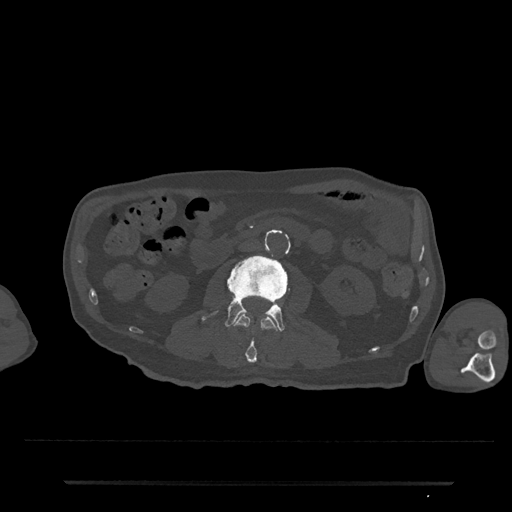
CT including the spine, one axial slice. Position 17 of 797 along the scan axis. Reconstruction kernel Br40s/3. 120 kVp. Bone window (W 1800 / L 400 HU). 512 × 512 image matrix, field of view 427 × 427 mm. Patient: male, 74 years. From the clinical record (not read from this slice): primary cancer: prostate.
Outlined on this slice (semi-automatically segmented with operator editing):
- L2 vertebra: bounding box [x1, y1, x2, y2] px = [234, 314, 278, 363]
- L3 vertebra: [201, 255, 290, 332]